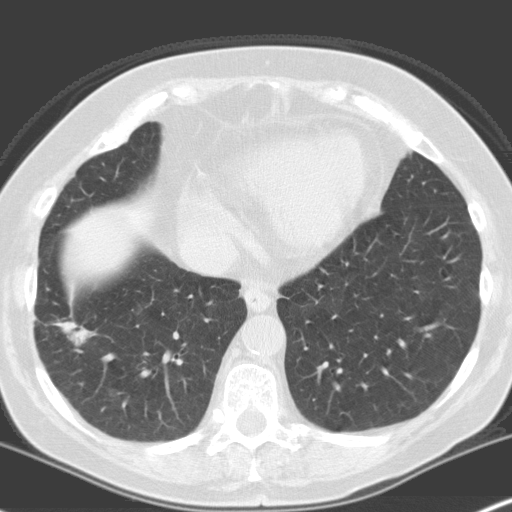
Low-dose screening chest CT, one axial slice. Position 60 of 160 along the scan axis. 120 kVp. Lung window (W 1500 / L -600 HU). 3.2 mm slice thickness. 512 × 512 image matrix.
Structures marked on this image (expert manual segmentation):
- lesion 1 (tumor, lower lobe of right lung): bounding box <57,320,92,345> (left, top, right, bottom; pixels)